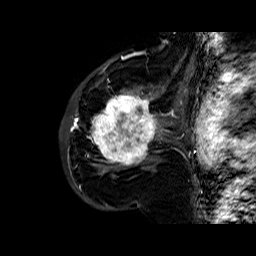
Breast MRI (dynamic contrast-enhanced), one sagittal slice; slice 40 of 60 in the series (ordered by position); dynamic contrast-enhanced series, time point 2 of 6 at this slice position (early post-contrast); 1.5 T; TE 6.4 ms, TR 32.8 ms; 4 mm slice thickness; 256 × 256 image matrix, field of view 200 × 200 mm. Female patient. Case-level facts recorded for this patient, not image findings: setting: breast cancer imaged before/during neoadjuvant chemotherapy; receptor status: HR-positive, HER2-negative.
Annotated regions visible in this slice (semi-automatic segmentation, software-assisted and operator-edited):
- analysis volume of interest (the breast-tissue region the enhancement analysis was run in; not a lesion): bounding box [x1, y1, x2, y2] px = [86, 77, 163, 177]
- tumour enhancement mask (voxels above the 100 % enhancement threshold inside the analysis volume of interest): [91, 89, 162, 171]